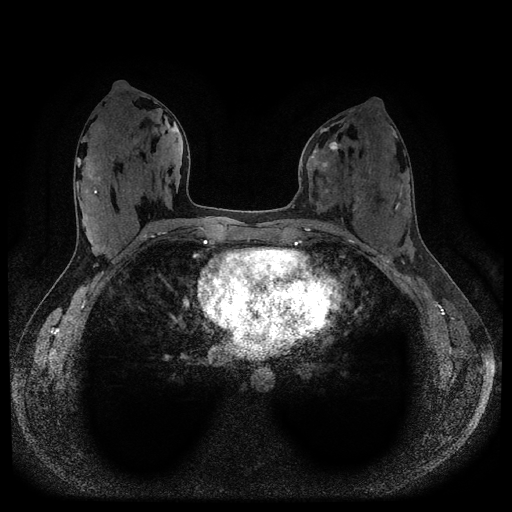
Breast MRI (dynamic contrast-enhanced, multi-phase), one axial slice; slice 48 of 116 in the series (ordered by position); dynamic contrast-enhanced series, time point 2 of 5 at this slice position (early post-contrast); 1.5 T; TE 2.6 ms, TR 5.3 ms; 2 mm slice thickness; 512 × 512 image matrix, field of view 350 × 350 mm. Patient: female, 33 years.
Outlined on this slice (semi-automatically segmented with operator editing):
- breast lesion (labelled 'tumour' in the annotation; benign lesions carry a separate 'benign' label): bounding box [x1, y1, x2, y2] px = [329, 141, 341, 152]